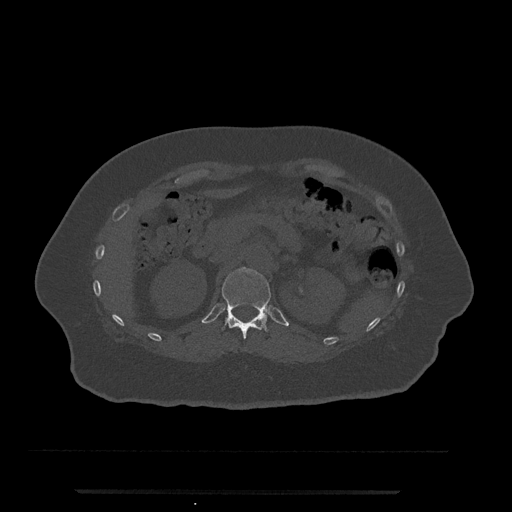
CT including the spine, one axial slice; slice 165 of 797 in the series (ordered by position); reconstruction kernel Br40s/3; 120 kVp; bone window (W 1800 / L 400 HU); 0.5 mm slice thickness; 512 × 512 image matrix, field of view 440 × 440 mm. Patient: female, 51 years. From the clinical record (not read from this slice): primary cancer: neuro.
Structures marked on this image (semi-automatically segmented with operator editing):
- T12 vertebra: bounding box (x1, y1, x2, y2) in pixels: (222, 268, 271, 339)